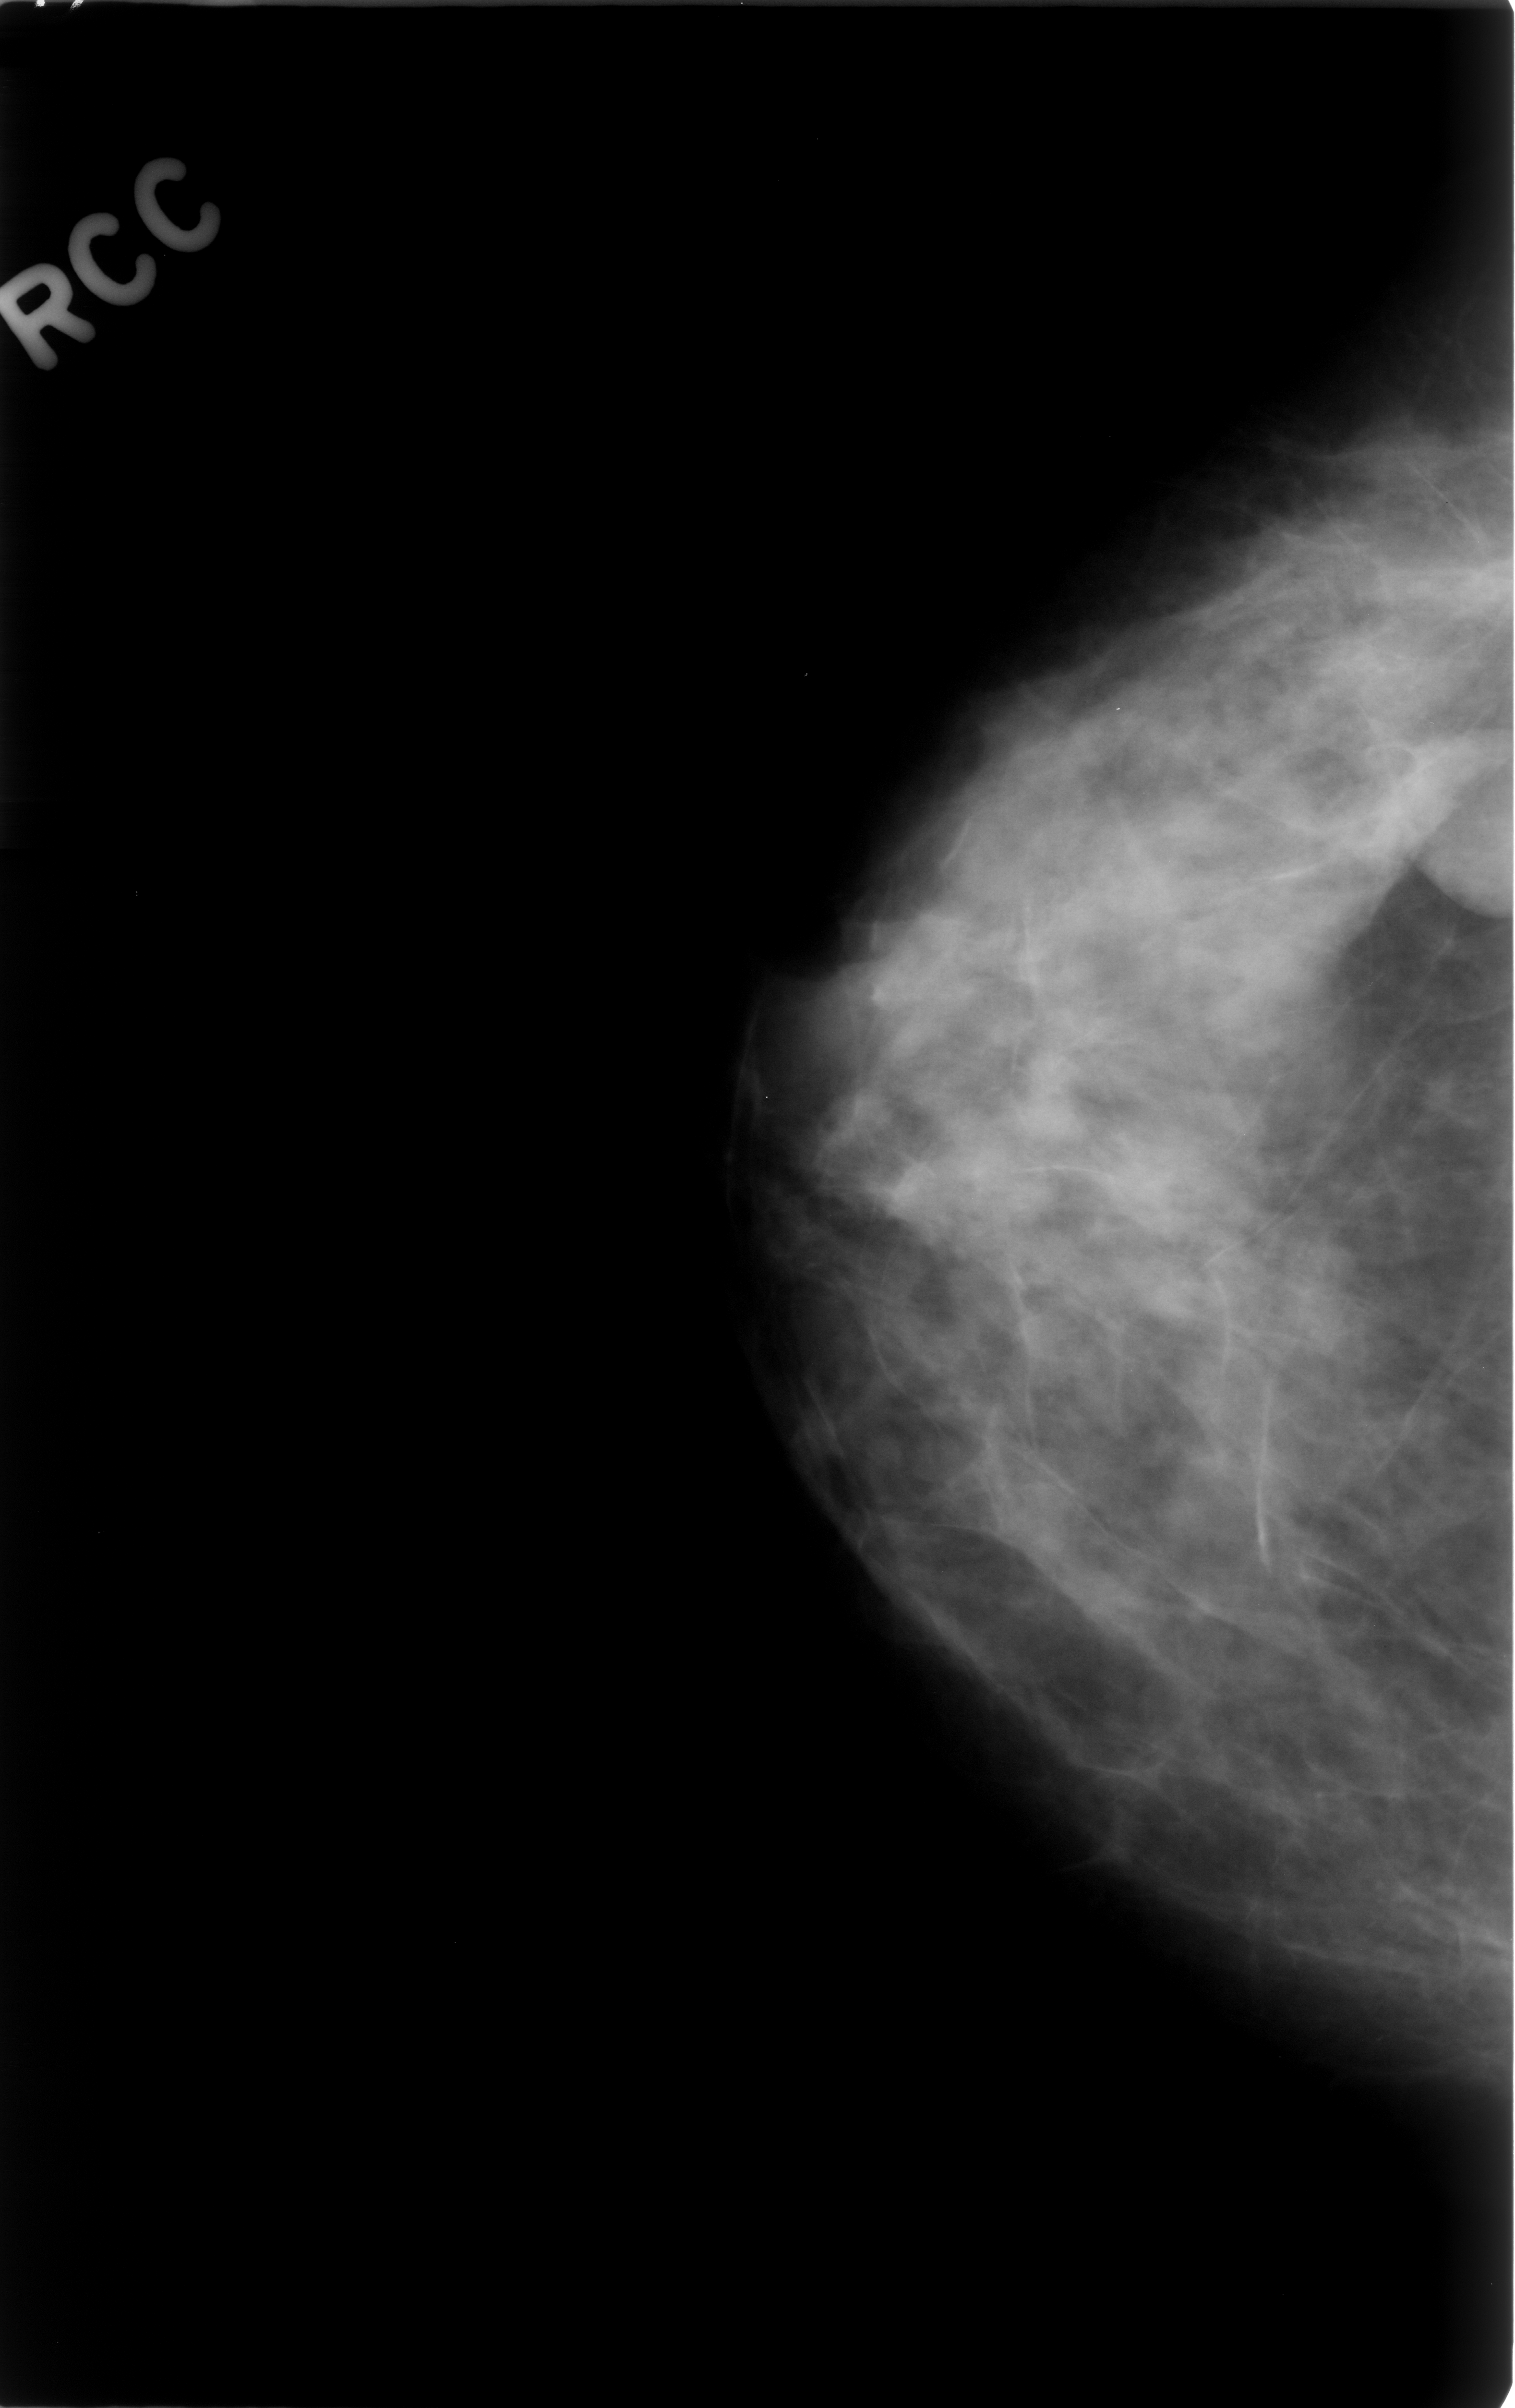
Scanned film-screen mammogram; right breast; craniocaudal (CC) view; breast composition: heterogeneously dense (BI-RADS density category 3 of 4); 1515 × 2408 image matrix.
Marked abnormalities (boxes around the expert regions of interest):
- mass, shape round, margins circumscribed; BI-RADS assessment category 3; subtlety rating 4 on a 1 (subtle) to 5 (obvious) scale; pathology result (as recorded, not read from the image): benign: box from (x=1413, y=727) to (x=1515, y=923) px